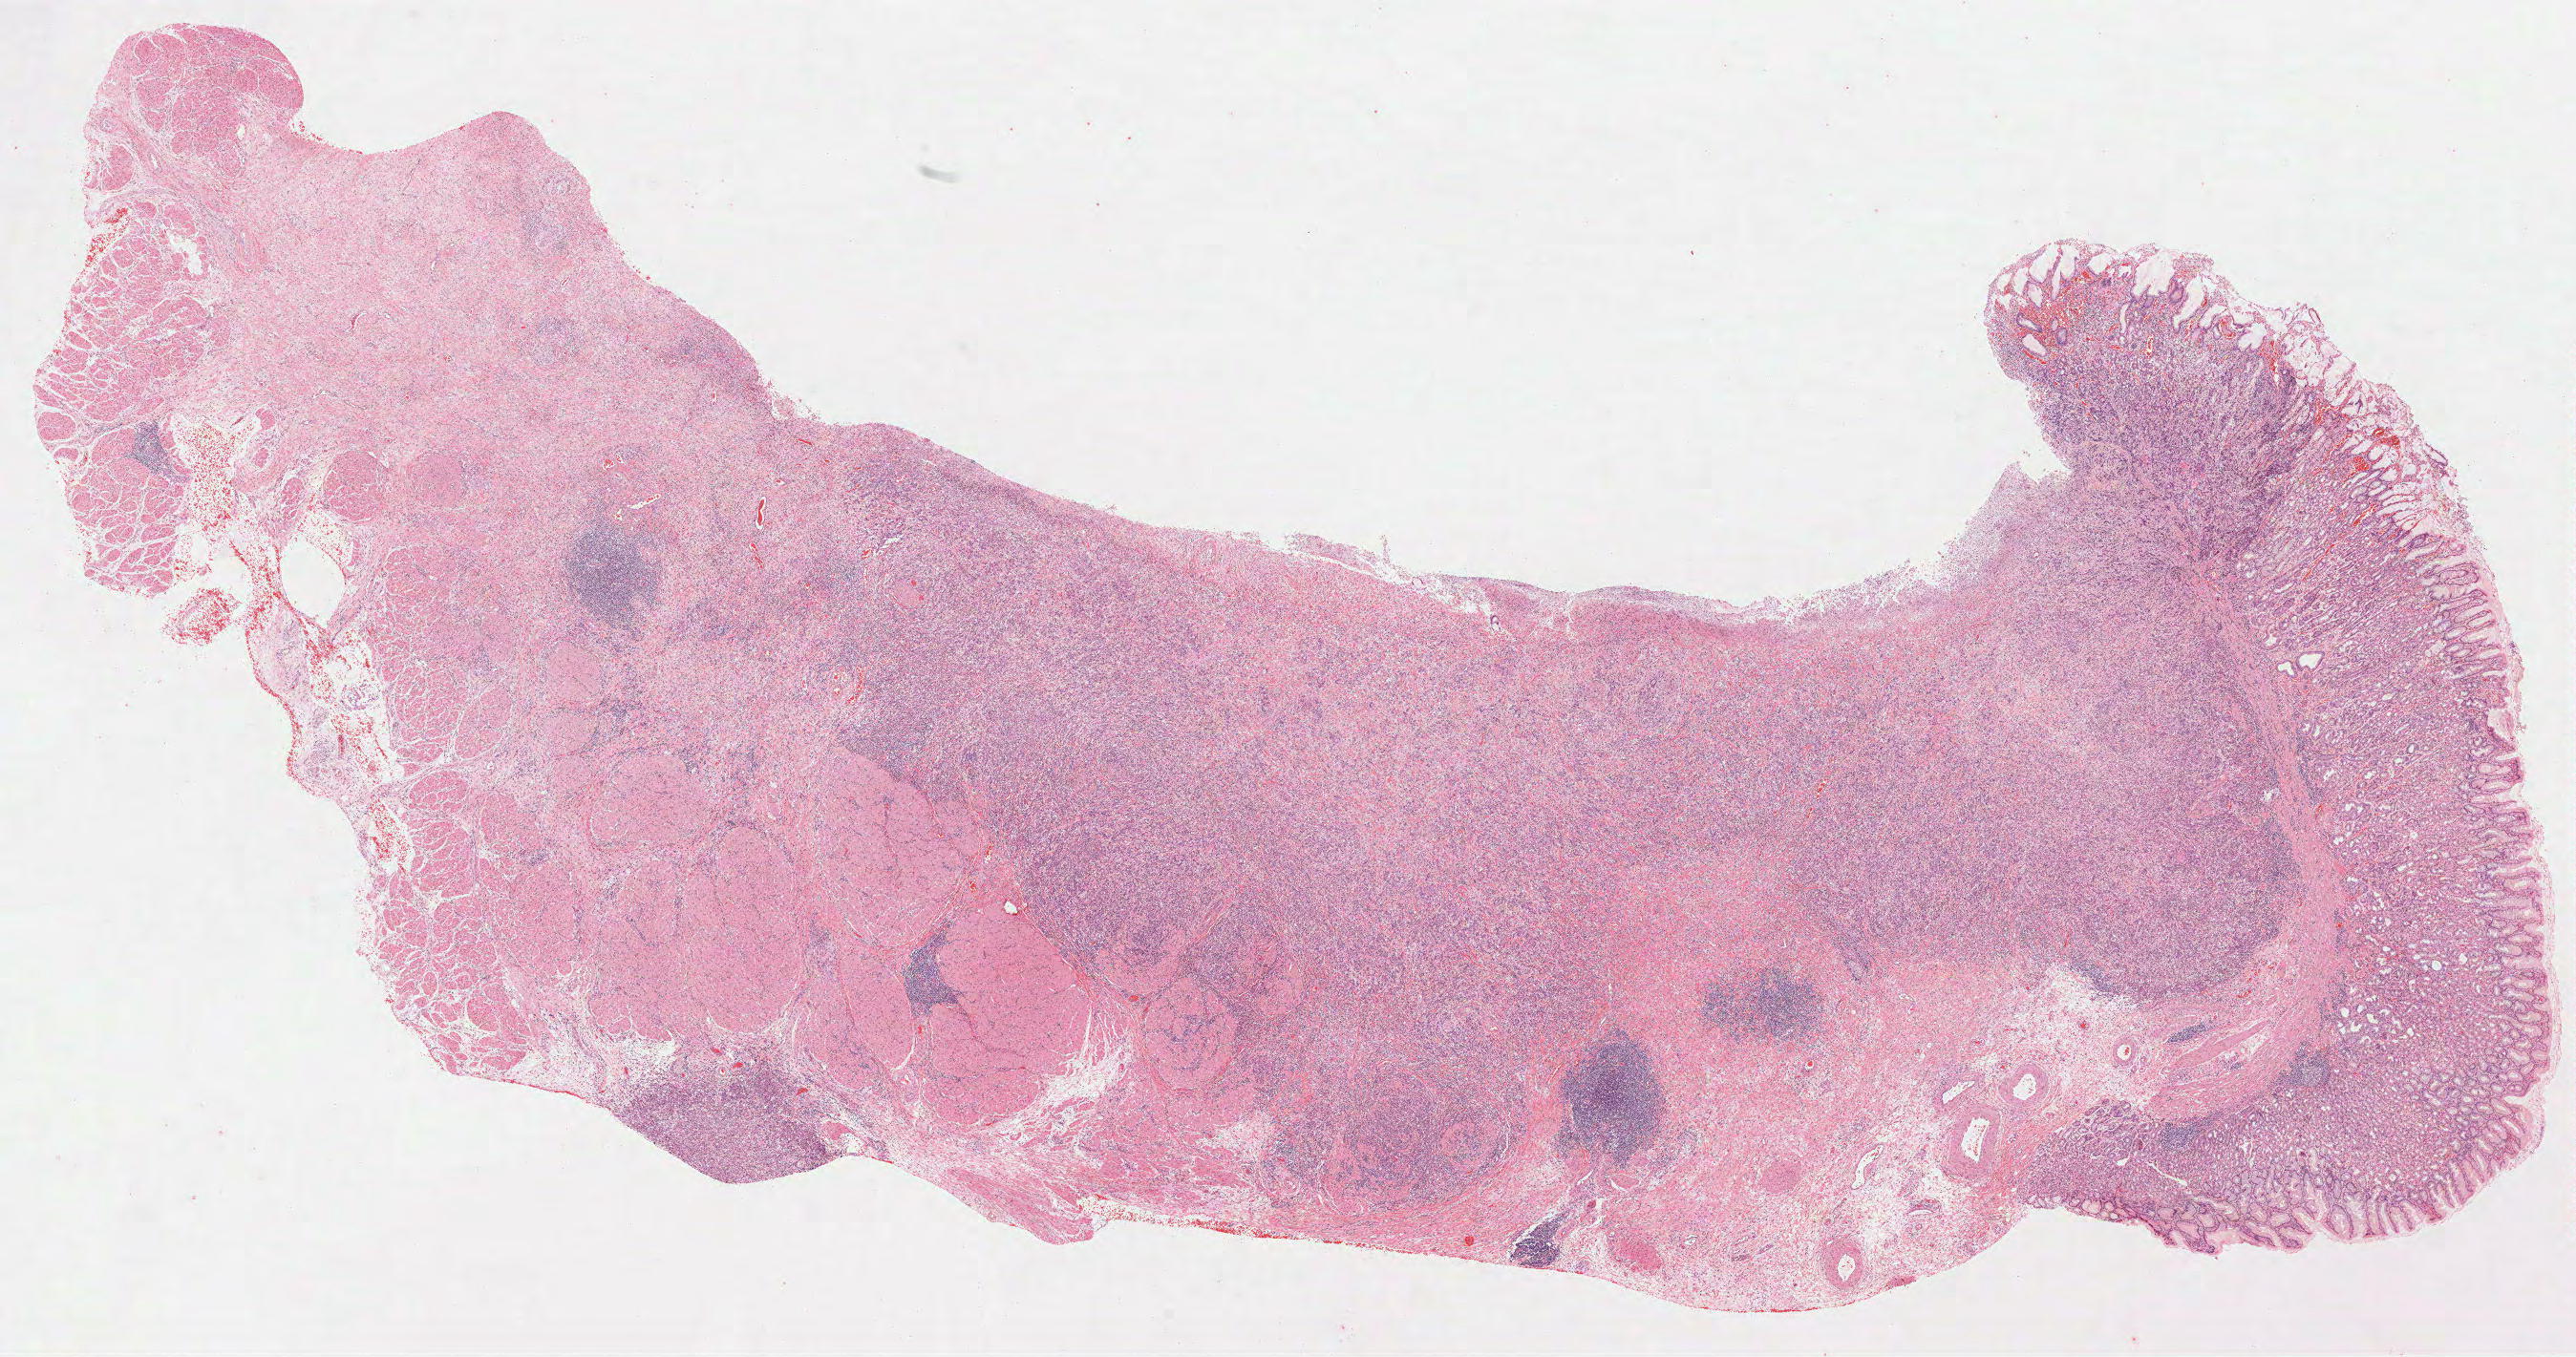
Digitized Hematoxylin and eosin (H&E) stained tissue section (whole slide) — shown as a low-resolution overview of the whole scanned area (about 21.8 x 11.5 mm). Formalin-fixed paraffin-embedded (FFPE) diagnostic section. Stomach, primary tumour sample. Female, age 55 years at initial diagnosis. Histologic grade: G3 (poorly differentiated).
Lymph nodes positive (case pathology): 0 of 6 examined. AJCC pathologic stage: IIB (7th edition). TNM: T4a N0 M0. Histologic diagnosis: Adenocarcinoma, NOS (fundus of stomach).